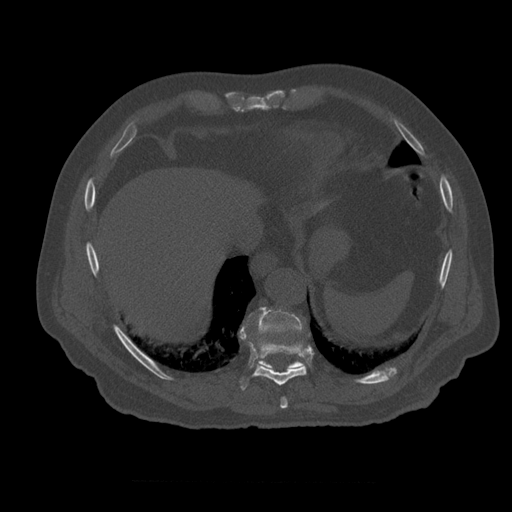
CT including the spine, one axial slice; slice 316 of 399 in the series (ordered by position); reconstruction kernel STANDARD; 120 kVp; bone window (W 1800 / L 400 HU); 1.25 mm slice thickness; 512 × 512 image matrix. Patient age 73 years. From the clinical record (not read from this slice): primary cancer: prostate; vertebrae with lytic lesions (as recorded): L2.
Outlined on this slice (semi-automatic segmentation, software-assisted and operator-edited):
- T10 vertebra: bounding box (x1, y1, x2, y2) in pixels: (257, 307, 305, 370)
- T8 vertebra: (281, 397, 288, 409)
- T9 vertebra: (240, 326, 307, 391)